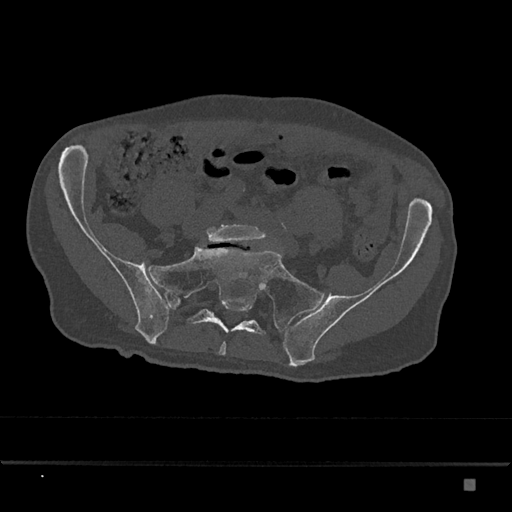
CT including the spine, one axial slice. Position 216 of 797 along the scan axis. Reconstruction kernel Br40s/3. 120 kVp. Bone window (W 1800 / L 400 HU). 0.5 mm slice thickness. 512 × 512 image matrix, field of view 390 × 390 mm. Patient: male, 72 years. Case-level facts recorded for this patient, not image findings: primary cancer: prostate.
Outlined on this slice (semi-automatically segmented with operator editing):
- L5 vertebra: bounding box (x1, y1, x2, y2) in pixels: (206, 224, 266, 243)